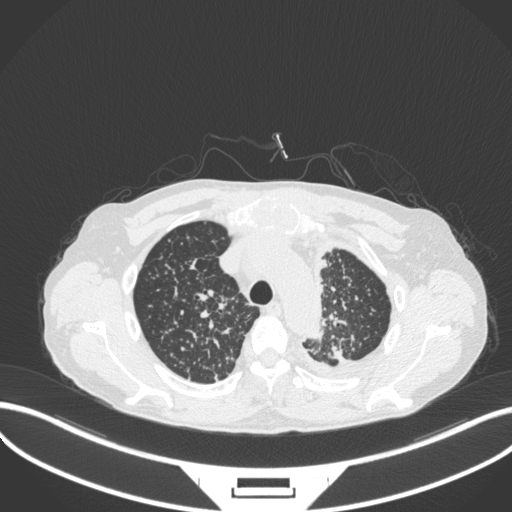
Chest CT, one axial slice. Slice 278 of 319 in the series (ordered by position). Reconstruction kernel B31f. Lung window (W 1500 / L -600 HU). 512 × 512 image matrix. Male patient, age 58 years. From the clinical record (not read from this slice): clinical TNM (as recorded): T1c N3 M1.
Annotated regions visible in this slice (bounding box drawn by a radiologist):
- lung tumour (recorded histology: adenocarcinoma): bounding box [x1, y1, x2, y2] px = [325, 339, 351, 362]